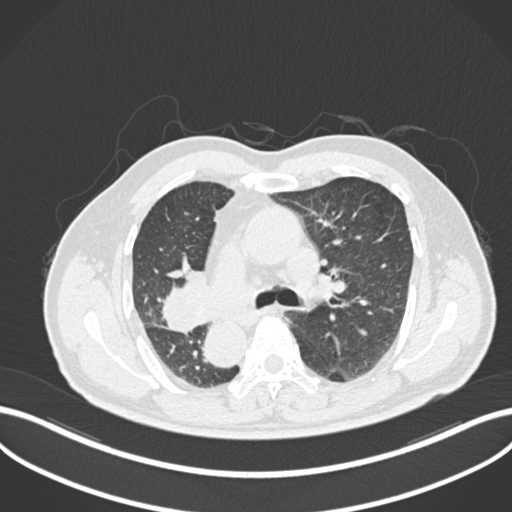
Chest CT, one axial slice; position 149 of 206 along the scan axis; reconstruction kernel B30f; lung window (W 1500 / L -600 HU); 1 mm slice thickness; 512 × 512 image matrix, field of view 400 × 400 mm. Male patient, age 67 years. From the clinical record (not read from this slice): clinical TNM (as recorded): T2a N0 M0.
Annotated regions visible in this slice (bounding box drawn by a radiologist):
- lung tumour (recorded histology: squamous cell carcinoma): bounding box [x1, y1, x2, y2] px = [158, 263, 211, 338]